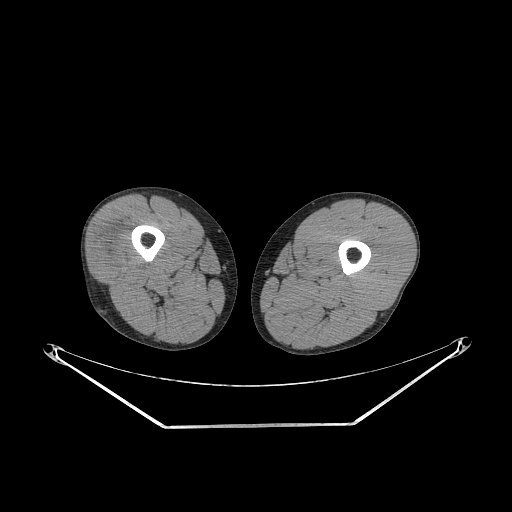
CT of an extremity soft-tissue mass (from a PET/CT study), one axial slice. Slice 222 of 267 in the series (ordered by position). Reconstruction kernel STANDARD. 140 kVp. Soft-tissue window (W 400 / L 40 HU). 512 × 512 image matrix, field of view 500 × 500 mm. Male patient. From the clinical record (not read from this slice): histological type: poorly differentiated synovial sarcoma; grade: high; site of the primary tumour: right buttock.
Structures marked on this image (expert contour drawn on MRI and transferred to this co-registered scan by the dataset authors):
- gross tumour volume including surrounding oedema: bounding box (x1, y1, x2, y2) in pixels: (98, 235, 136, 271)